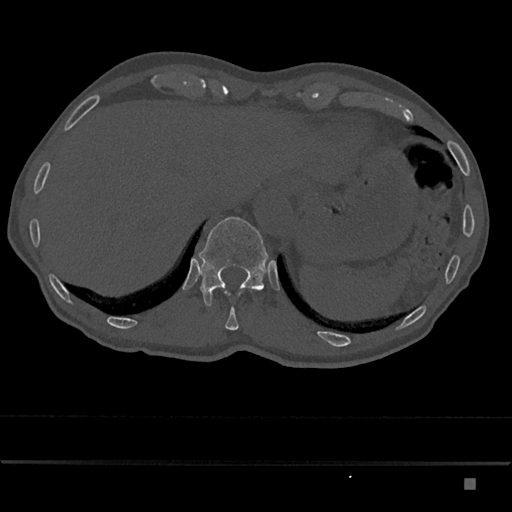
CT including the spine, one axial slice. Bone window (W 1800 / L 400 HU). 512 × 512 image matrix, field of view 390 × 390 mm. Male patient, age 72 years. From the clinical record (not read from this slice): primary cancer: prostate.
Structures marked on this image (semi-automatically segmented with operator editing):
- T11 vertebra: box from (x=225, y=307) to (x=239, y=330) px
- T12 vertebra: (x=198, y=217)–(x=269, y=306)